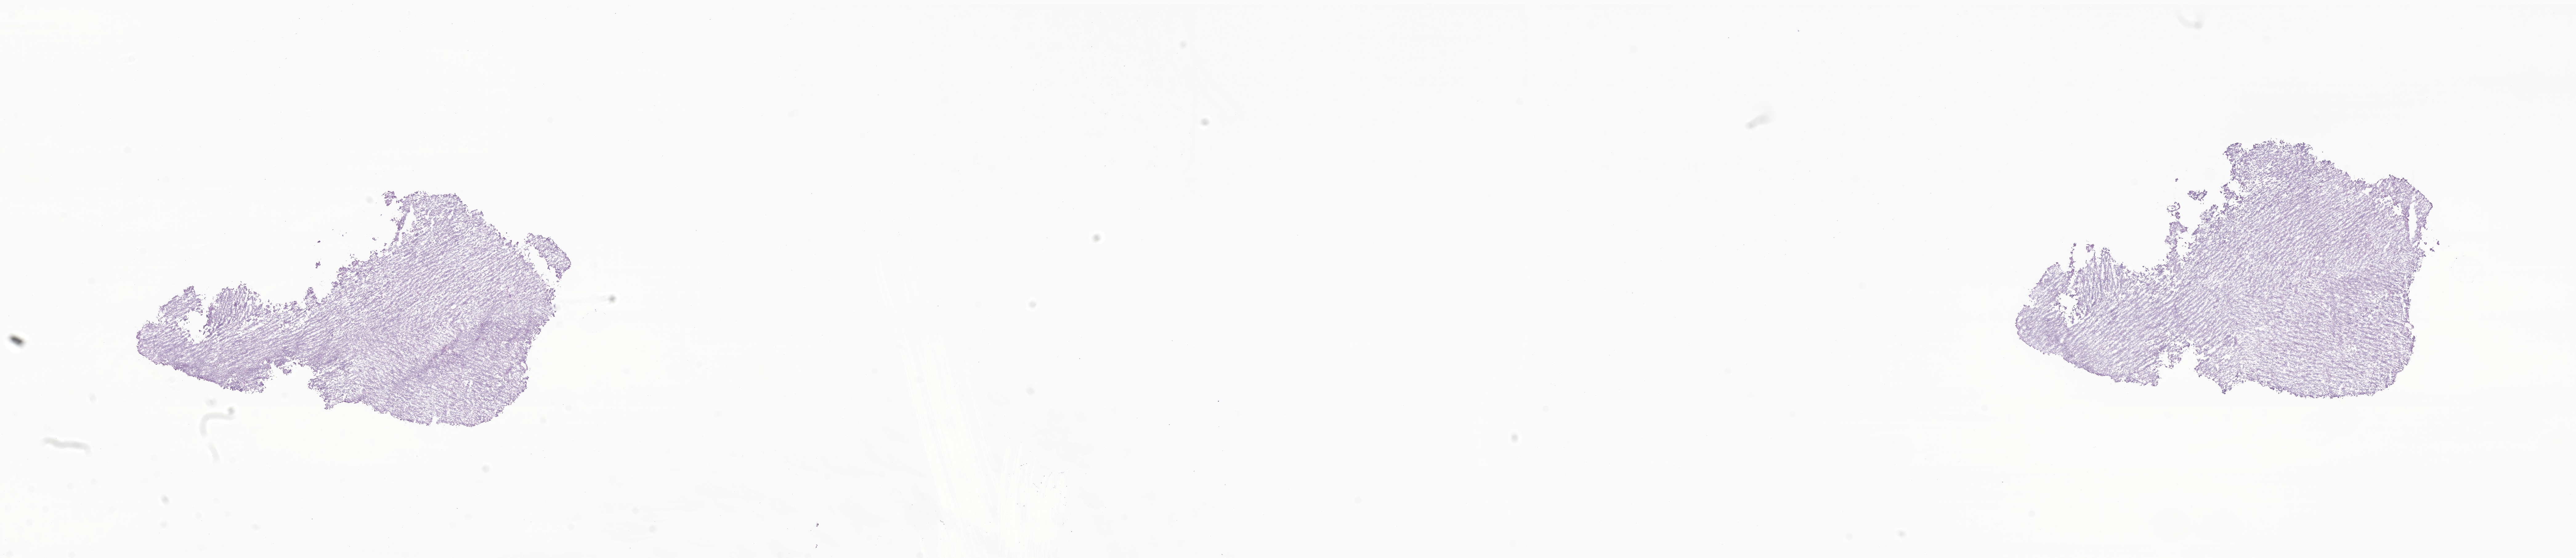
Whole-slide image, hematoxylin and eosin (H&E) stain of tumor tissue from the brain — shown as a low-resolution overview of the whole scanned area (about 35.3 x 7.6 mm). Frozen section. Patient female; age 79 months (6 years 7 months).
- recorded diagnosis: Medulloblastoma, NOS